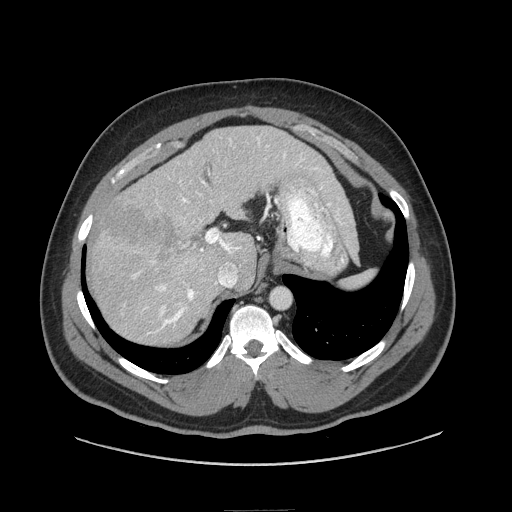
Contrast-enhanced abdominal CT (liver protocol), one axial slice; position 56 of 87 along the scan axis; reconstruction kernel STANDARD; 140 kVp; soft-tissue window (W 400 / L 40 HU); 512 × 512 image matrix, field of view 440 × 440 mm. From the clinical record (not read from this slice): diagnosis: hepatocellular carcinoma (patient treated with transarterial chemoembolisation; whether this scan precedes or follows treatment is not stated here); TNM stage (as recorded): Stage-II.
Structures marked on this image (semi-automatically segmented with operator editing):
- liver parenchyma outside the tumour (the mass and vessels are separate outlines, so this box may not span the whole liver): bounding box [x1, y1, x2, y2] px = [88, 126, 342, 344]
- mass: [100, 198, 179, 263]
- liver vessels: [133, 137, 323, 334]